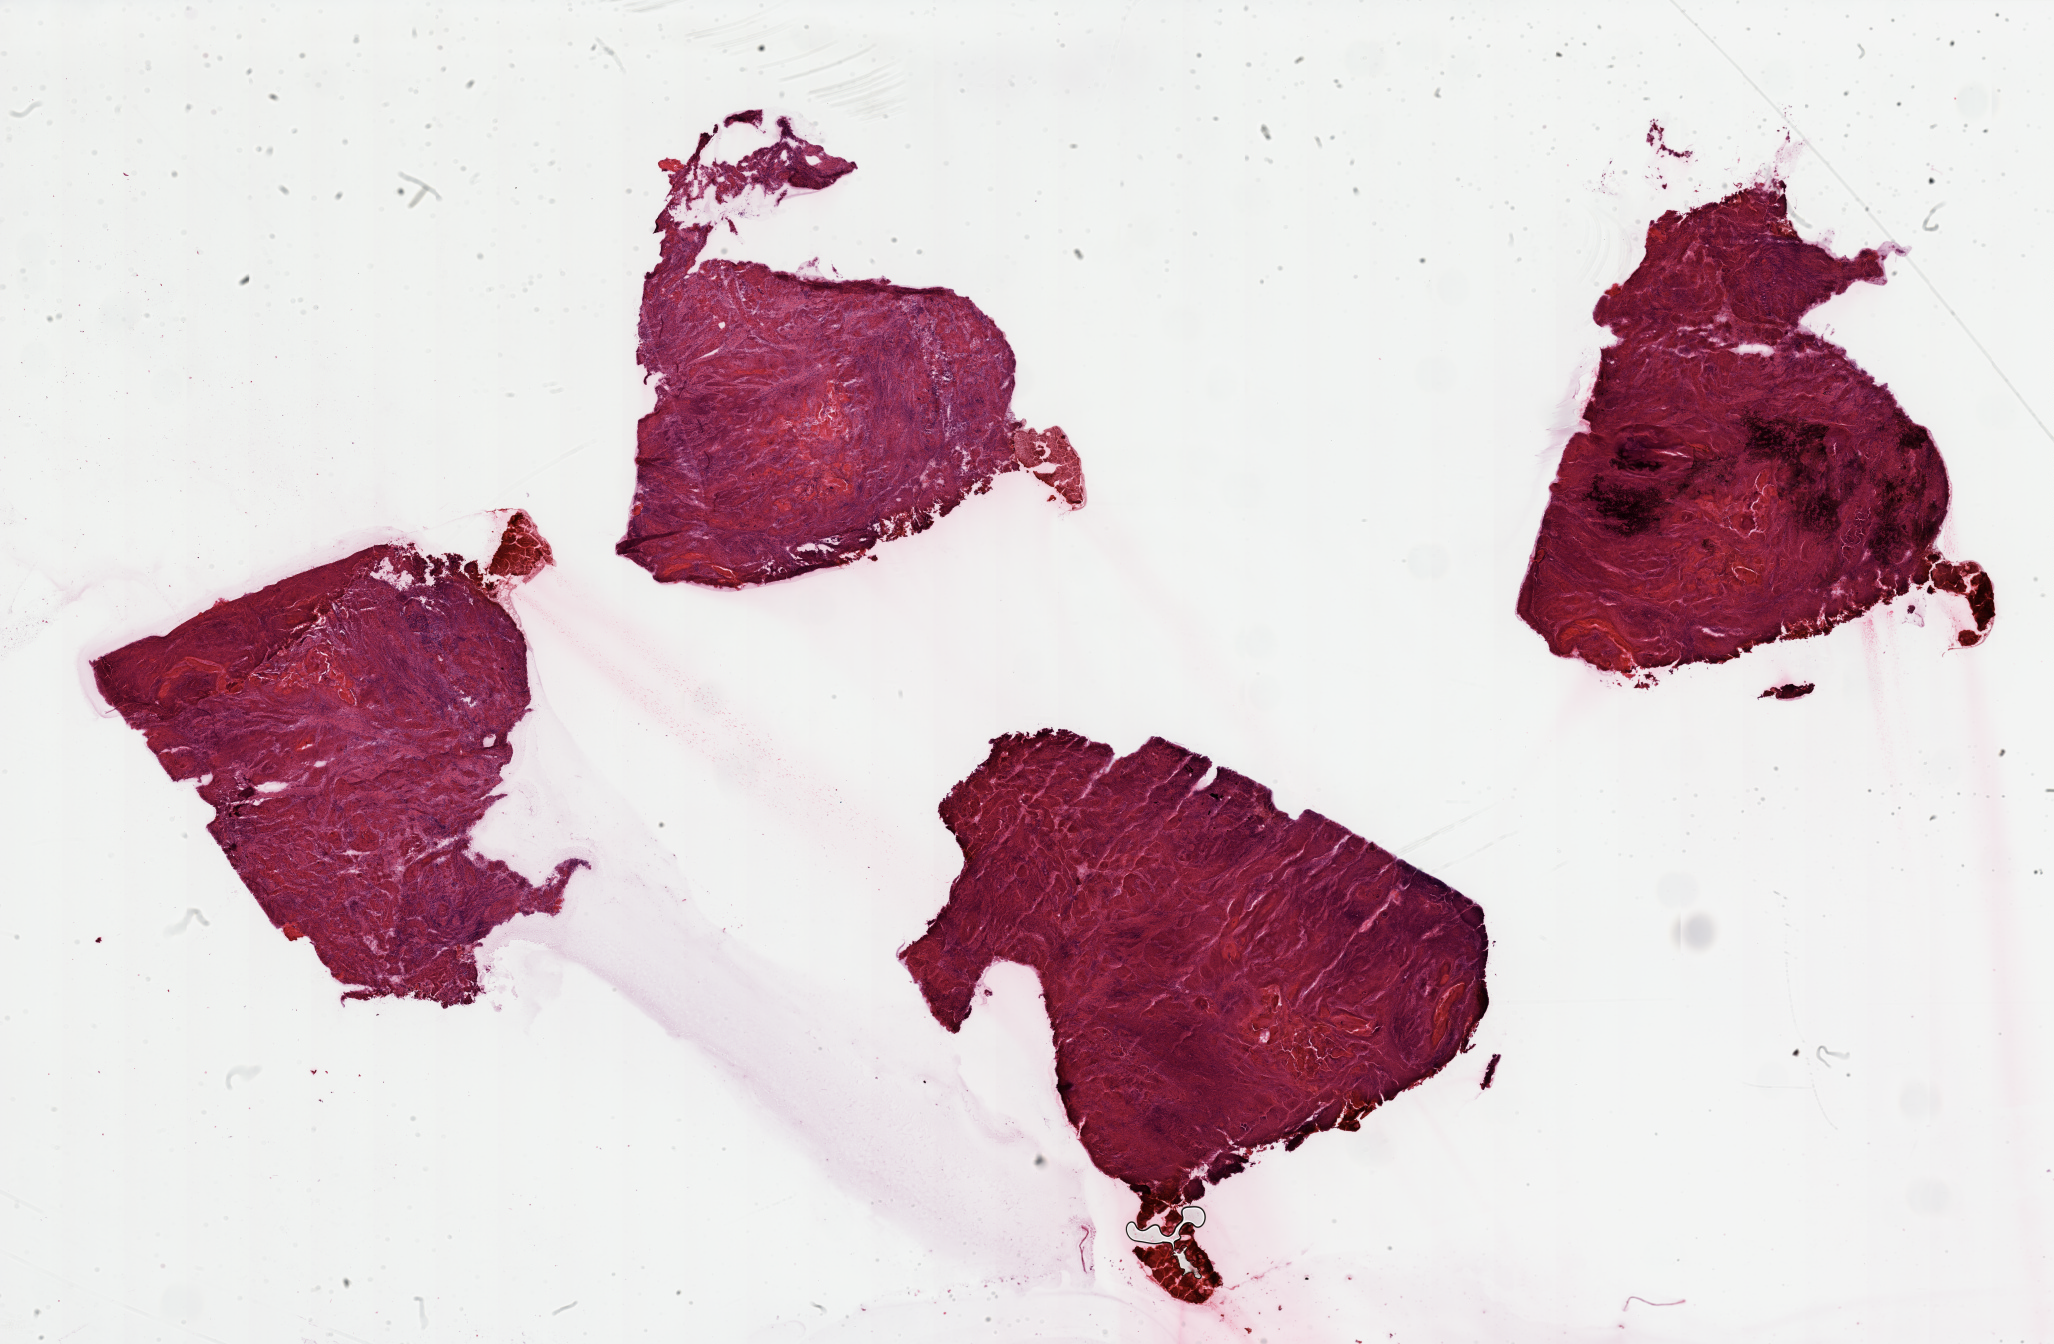
Digitized H&E-stained tissue section (whole slide) — a low-resolution overview of the entire scanned area, about 32.5 x 21.3 mm (acquisition: 20x scan), tumour tissue sample, sampled site: larynx. Male, 69 y/o. Histologic grade: G2 (moderately differentiated). Pathologist review of this section (percent, as recorded): tumour nuclei 85%, necrosis 15%.
* AJCC pathologic stage: II
* diagnosis: Squamous cell carcinoma, NOS (larynx, NOS)